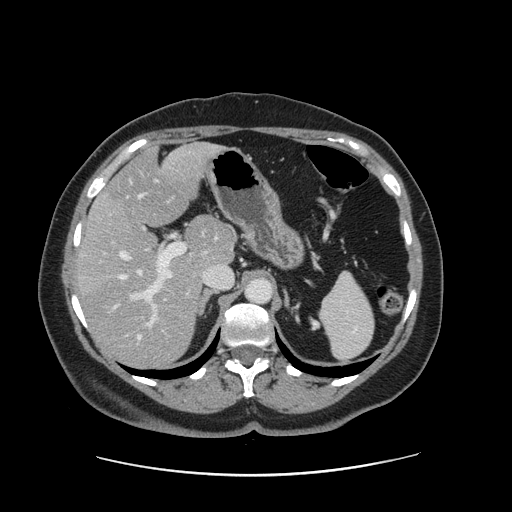
Contrast-enhanced abdominal CT, one axial slice. Position 93 of 161 along the scan axis. 120 kVp. Intravenous contrast given. Soft-tissue window (W 400 / L 40 HU). 2.5 mm slice thickness. 512 × 512 image matrix. Female patient, age 62 years. Case-level facts recorded for this patient, not image findings: diagnosis: colorectal cancer liver metastases, imaged before liver resection; multiple liver metastases: no; largest metastasis: 2.5 cm; disease in both lobes: no.
Annotated regions visible in this slice (expert manual segmentation):
- hepatic veins: bounding box <116,194,144,339> (left, top, right, bottom; pixels)
- liver: <80,144,234,366>
- planned liver remnant (the part of the liver to remain after resection): <105,144,233,267>
- portal vein (with intrahepatic branches): <127,243,186,336>